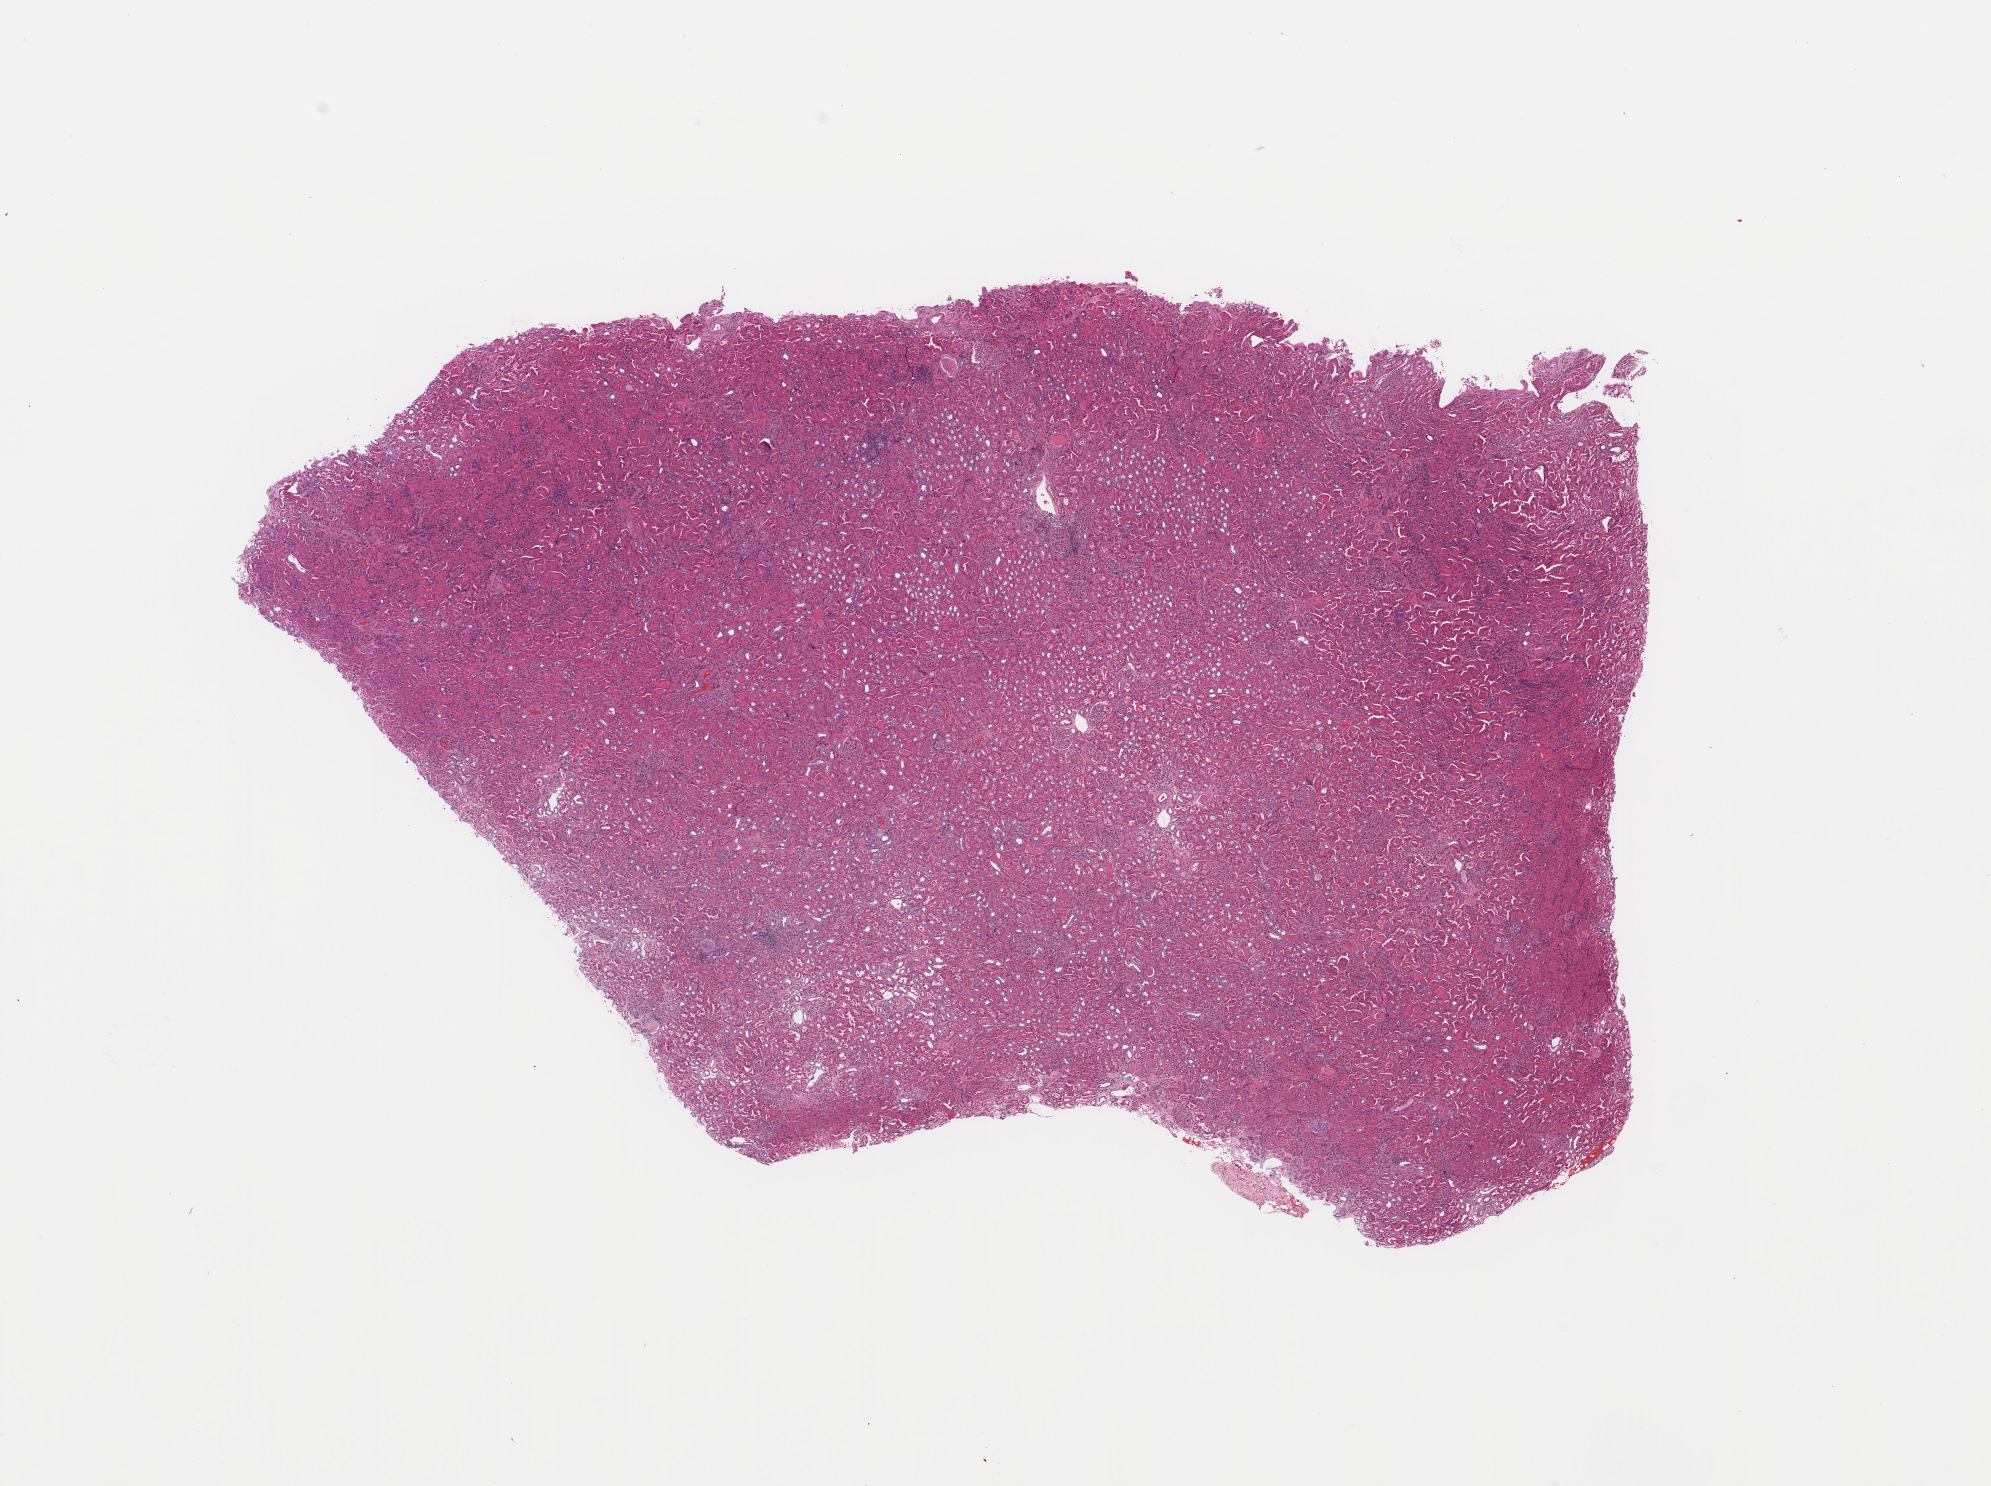
Digitized Hematoxylin and eosin (H&E) stained tissue section (whole slide) — whole scanned area (about 15.8 x 11.8 mm, from a 20x scan) shown as a low-resolution overview; normal (non-tumour) tissue sample, sampled site: kidney. Patient: male, age 61 years.
This section: normal (non-tumour) tissue from the same patient. Patient diagnosis: Renal cell carcinoma, NOS.